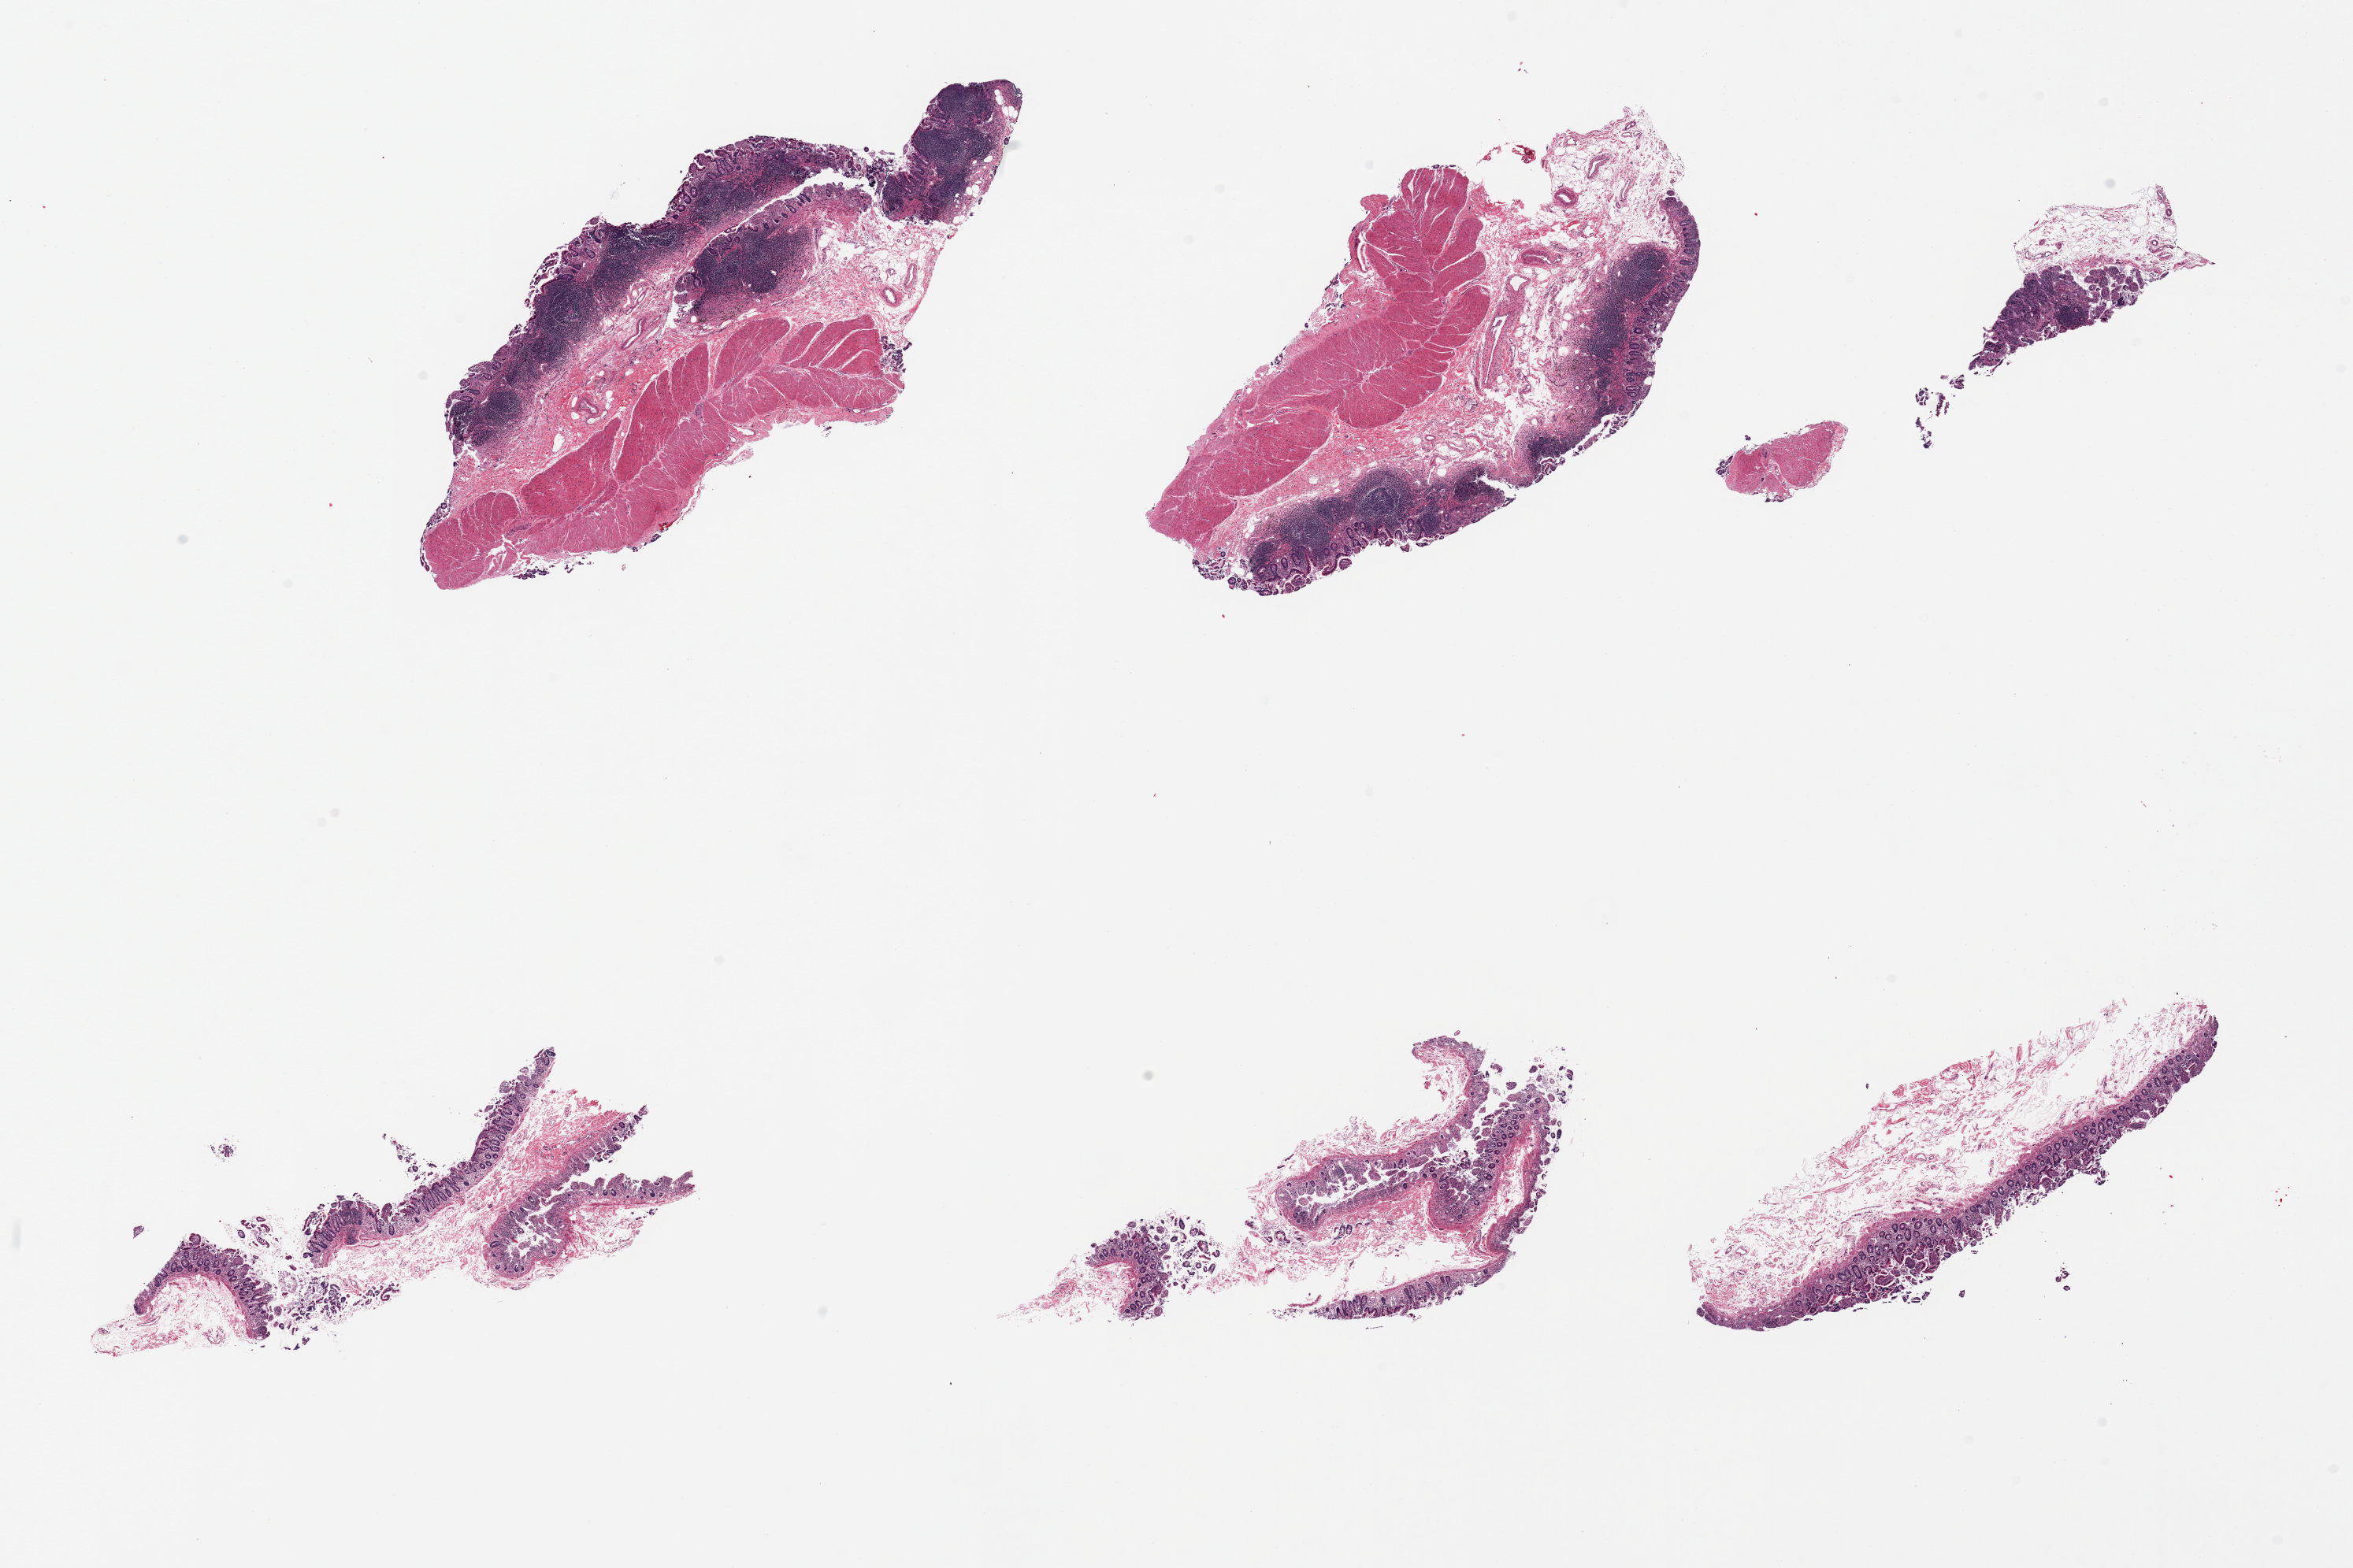
Digitized hematoxylin and eosin (H&E)-stained section, low-resolution overview of the scanned area, about 23.6 x 15.7 mm, PAXgene-fixed, paraffin-embedded tissue, section of ileum (target tissue), tissue donor sample. Donor: female.
* reviewer comment on this tissue sample: 6 pieces; 3 with mucosa/submucosa lack Peyer's patches, 3 with abundant lymphoid component include muscularis